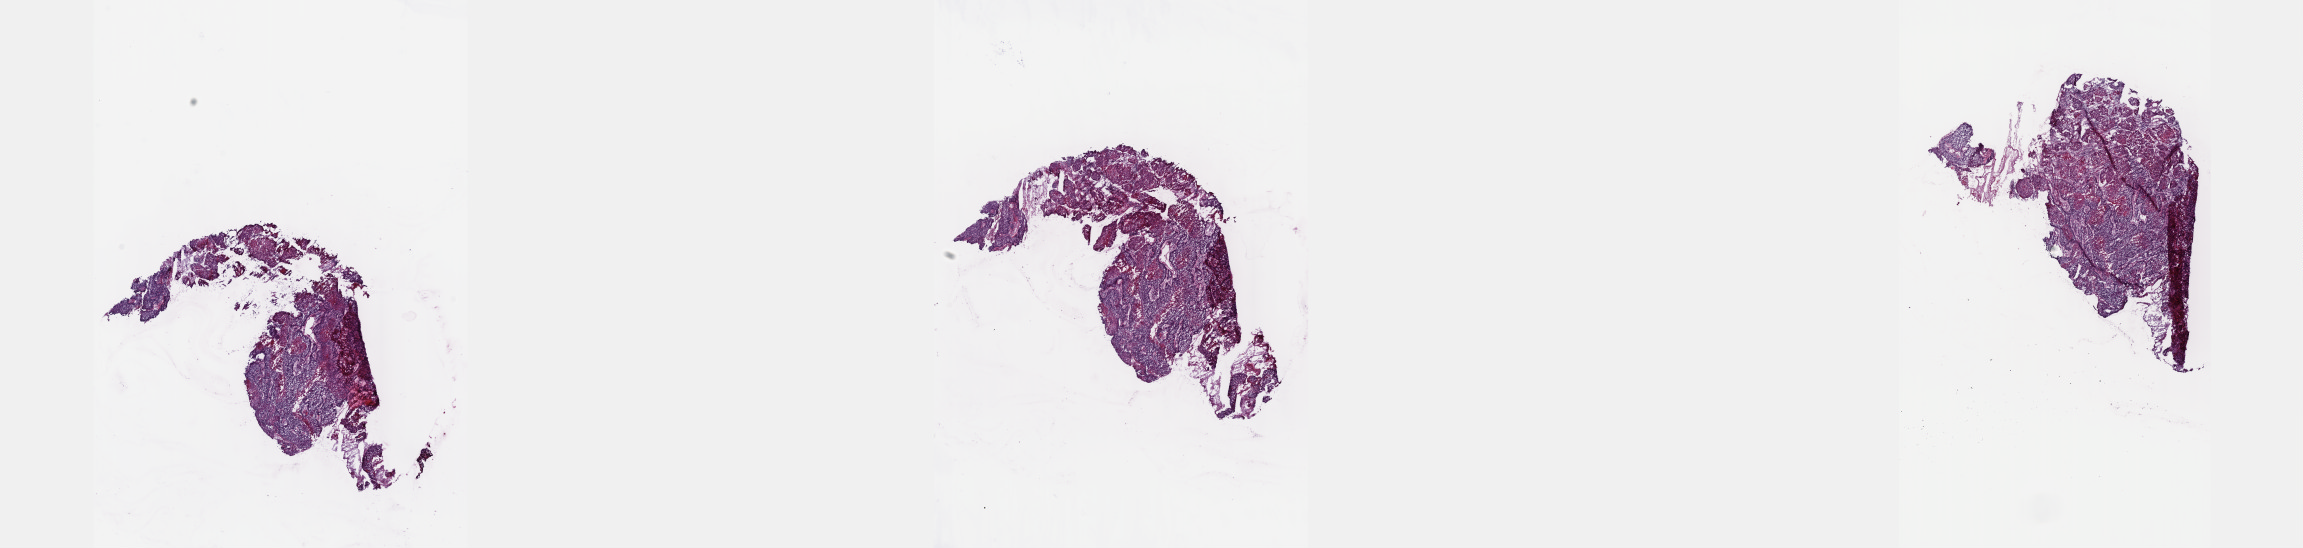
Whole-slide histology image, H&E, whole scanned area (about 37.2 x 8.9 mm, slide scanned at 40x) shown as a low-resolution overview. Frozen section from the top of the tissue portion. Cervix, primary tumour sample. Female patient; age at initial diagnosis 51 years. Histologic grade: G2 (moderately differentiated). Slide review estimates, as recorded: tumour cells 70%, tumour nuclei 70%, normal cells 0%, stromal cells 25%, necrosis 5%. Inflammatory infiltration, as recorded: lymphocyte infiltration 40%, monocyte infiltration 20%, neutrophil infiltration 20%.
* FIGO stage: IVA
* diagnosis: Squamous cell carcinoma, NOS (cervix uteri)